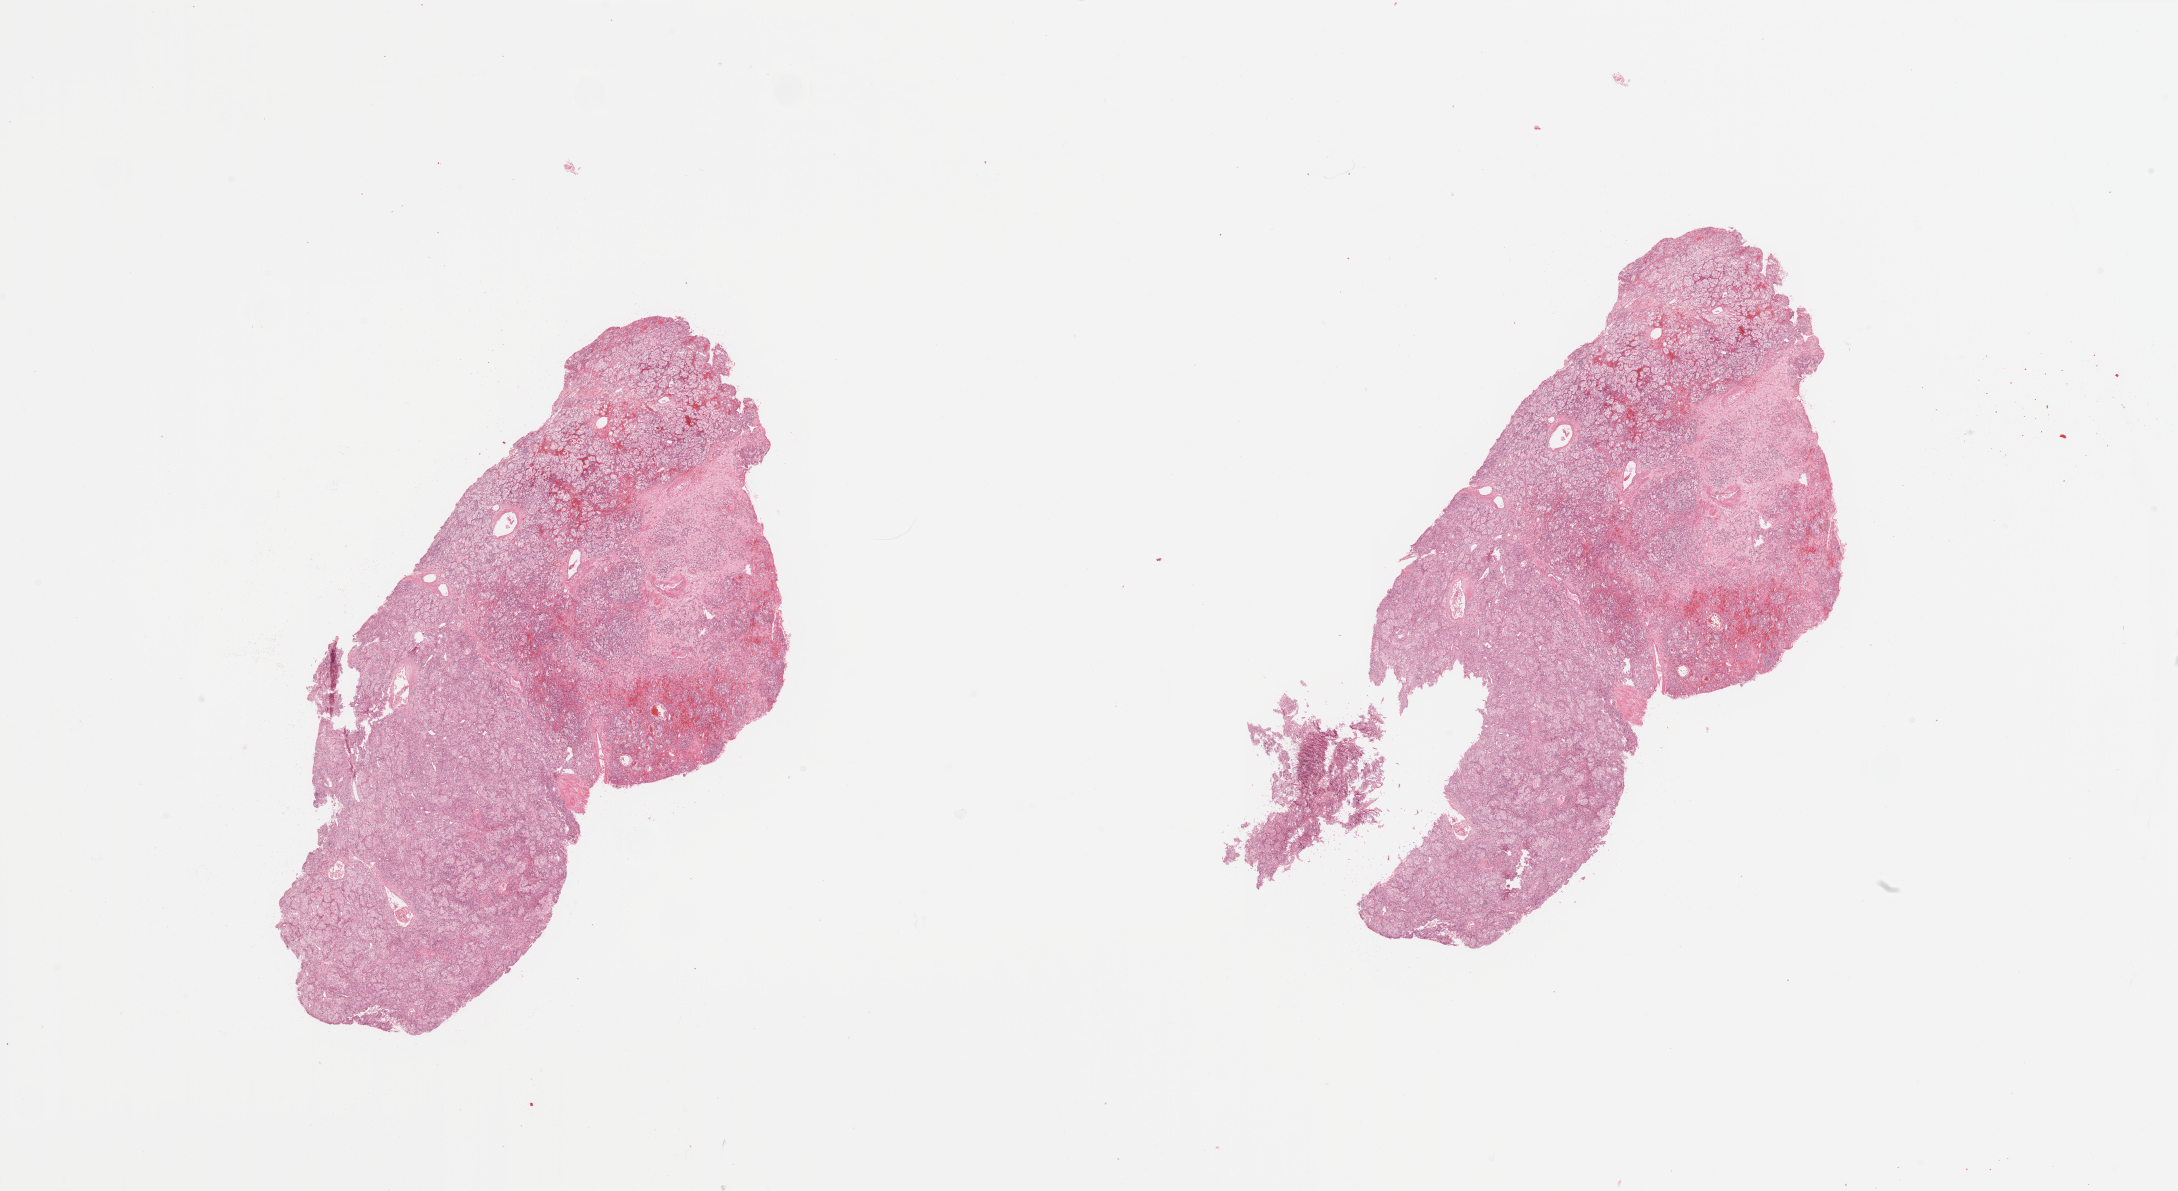
H&E whole-slide image, low-resolution overview of the scanned area, about 34.5 x 18.8 mm (slide scanned at 20x), tumour tissue sample, sampled site: kidney. Male, 56 y/o.
Histologic diagnosis: Renal cell carcinoma, NOS.